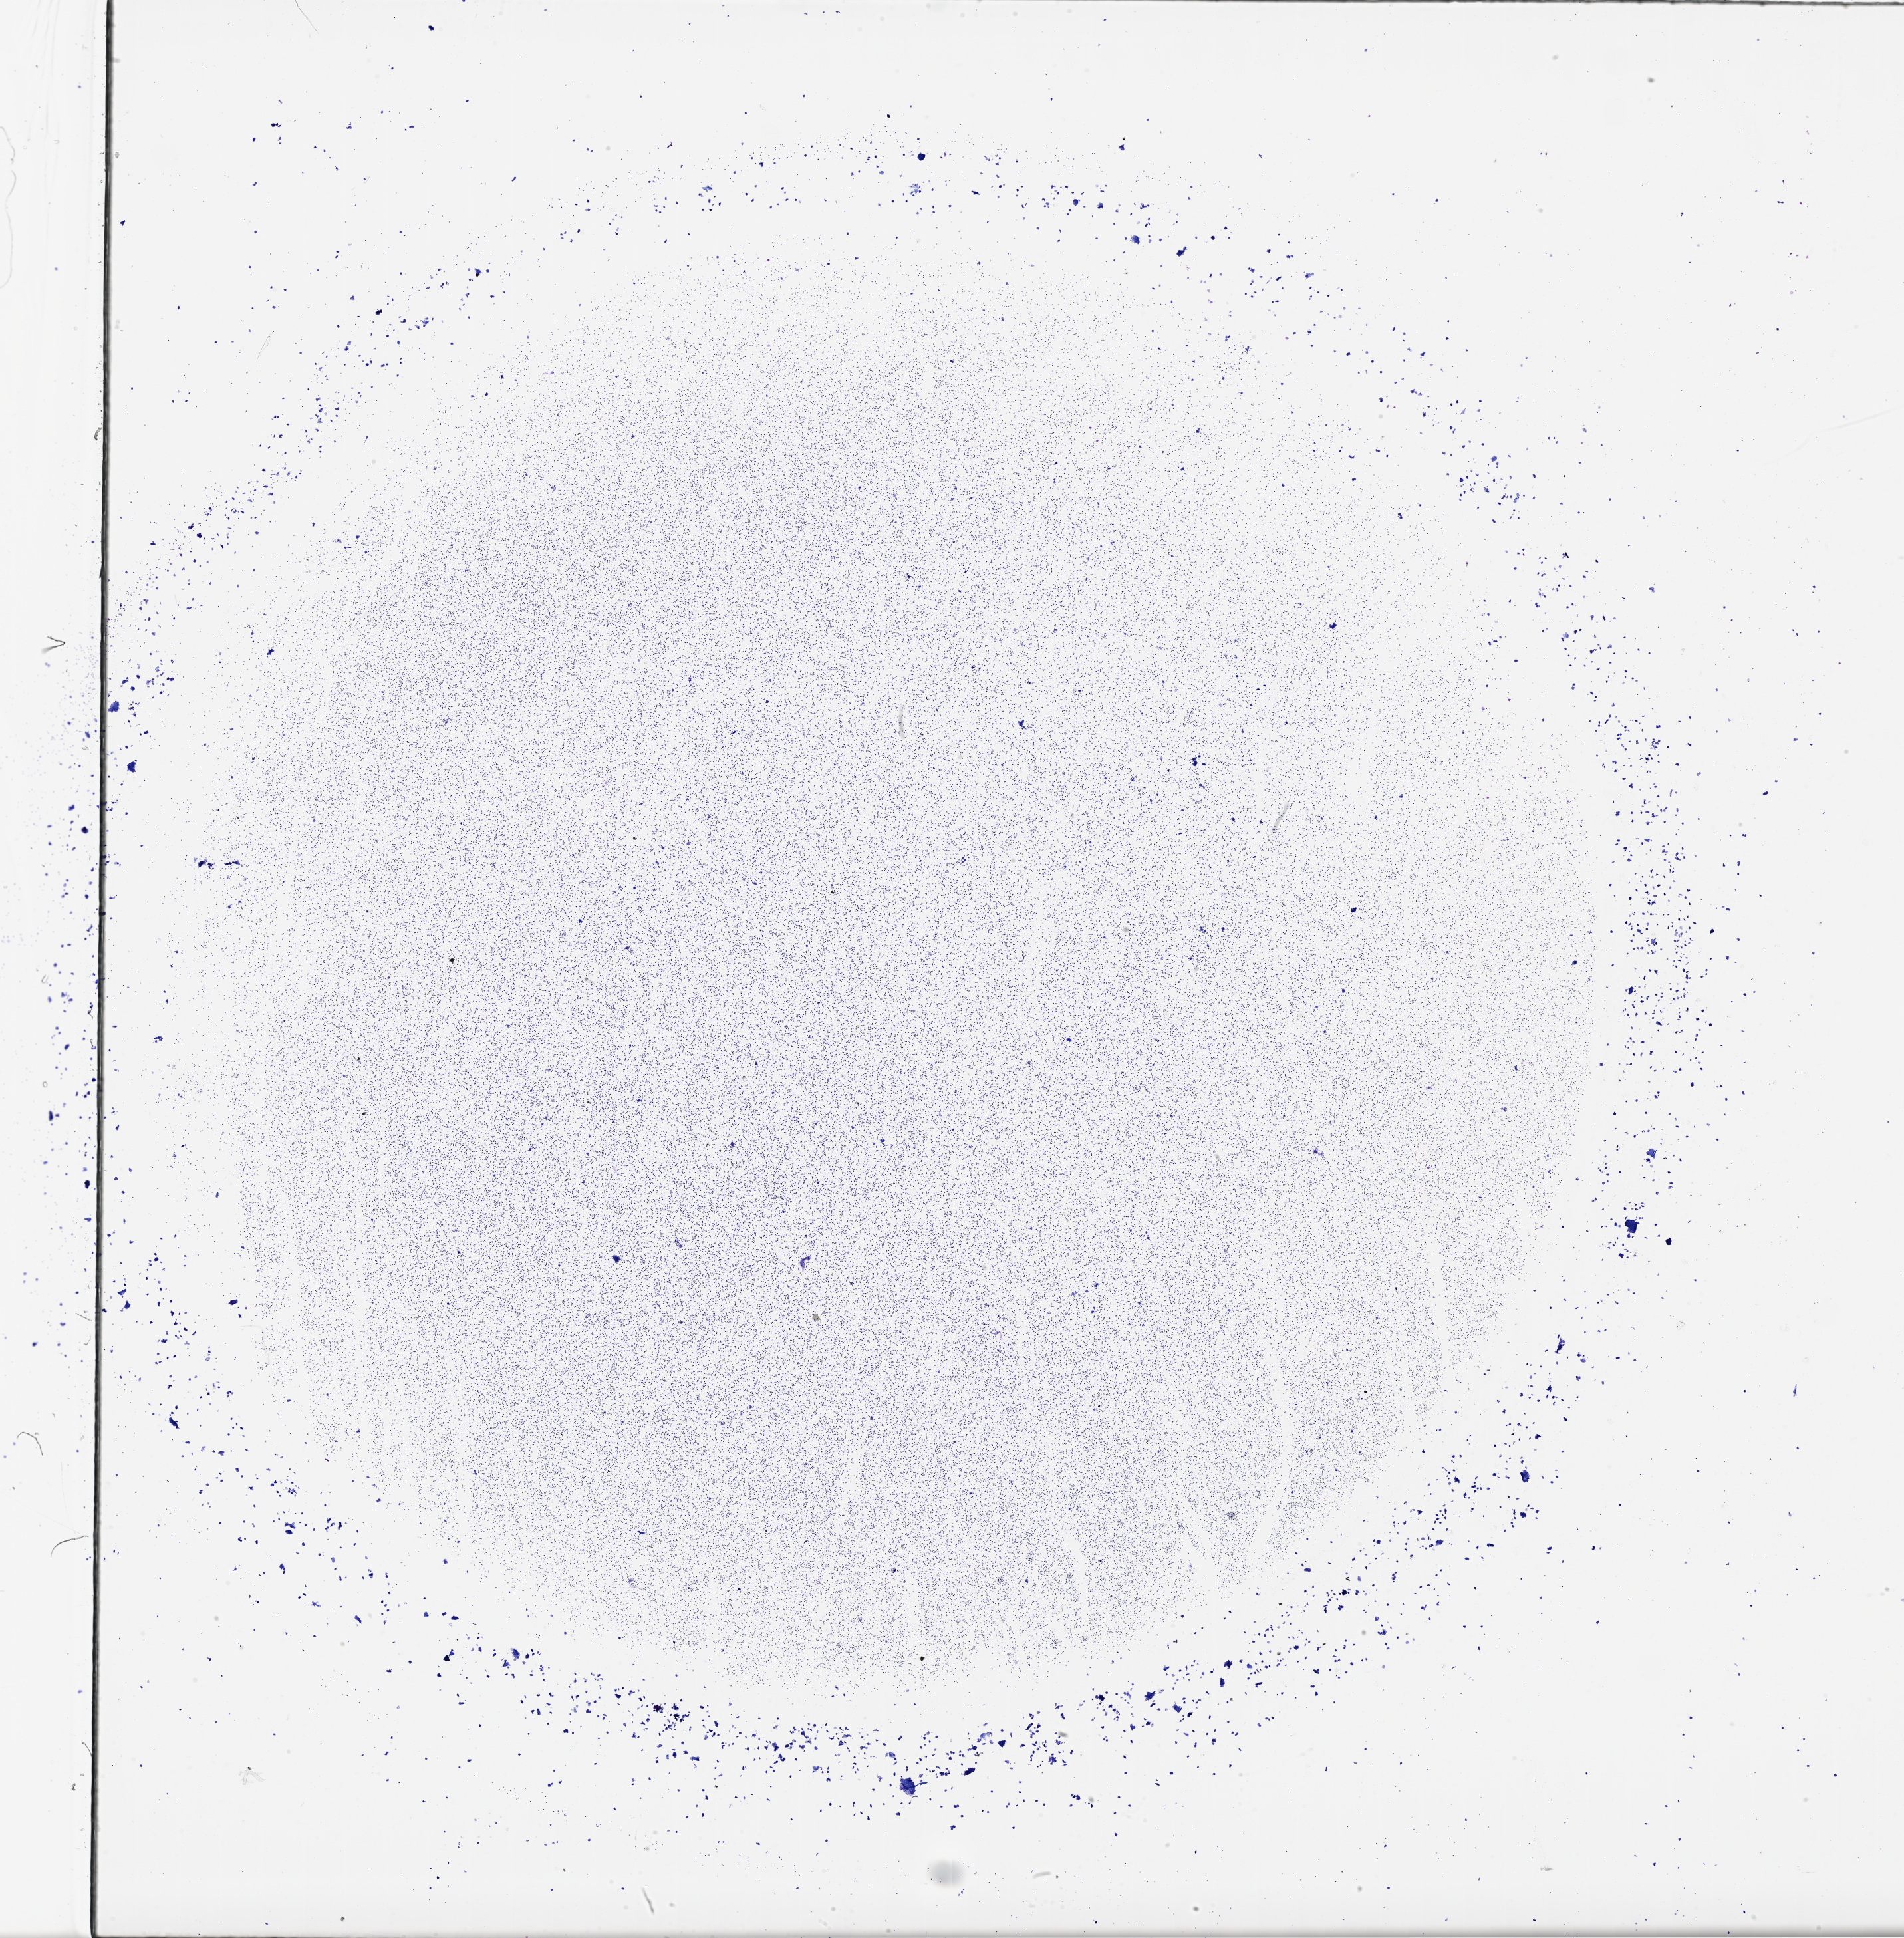
Digitized Hematoxylin and eosin (H&E) stained tissue section (whole slide) — shown as a low-resolution overview of the whole scanned area (about 23.1 x 23.5 mm); bone marrow (leukaemic) sample. Patient: female, age 40 years. Blasts: 20%.
* FAB classification: M5
* WHO classification: Acute monoblastic and monocytic leukemia
* diagnosis: Acute Myeloid Leukemia